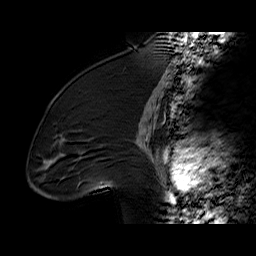
Breast MRI (dynamic contrast-enhanced), one sagittal slice. Position 37 of 60 along the scan axis. Dynamic contrast-enhanced series, time point 2 of 6 at this slice position (early post-contrast). 1.5 T. TE 6.2 ms, TR 32.4 ms. 4 mm slice thickness. 256 × 256 image matrix. Female patient. From the clinical record (not read from this slice): setting: breast cancer imaged before/during neoadjuvant chemotherapy; receptor status: triple-negative.
Structures marked on this image (semi-automatic segmentation, software-assisted and operator-edited):
- analysis volume of interest (the breast-tissue region the enhancement analysis was run in; not a lesion): bounding box (x1, y1, x2, y2) in pixels: (36, 97, 134, 196)
- tumour enhancement mask (voxels above the 100 % enhancement threshold inside the analysis volume of interest): (61, 138, 103, 183)